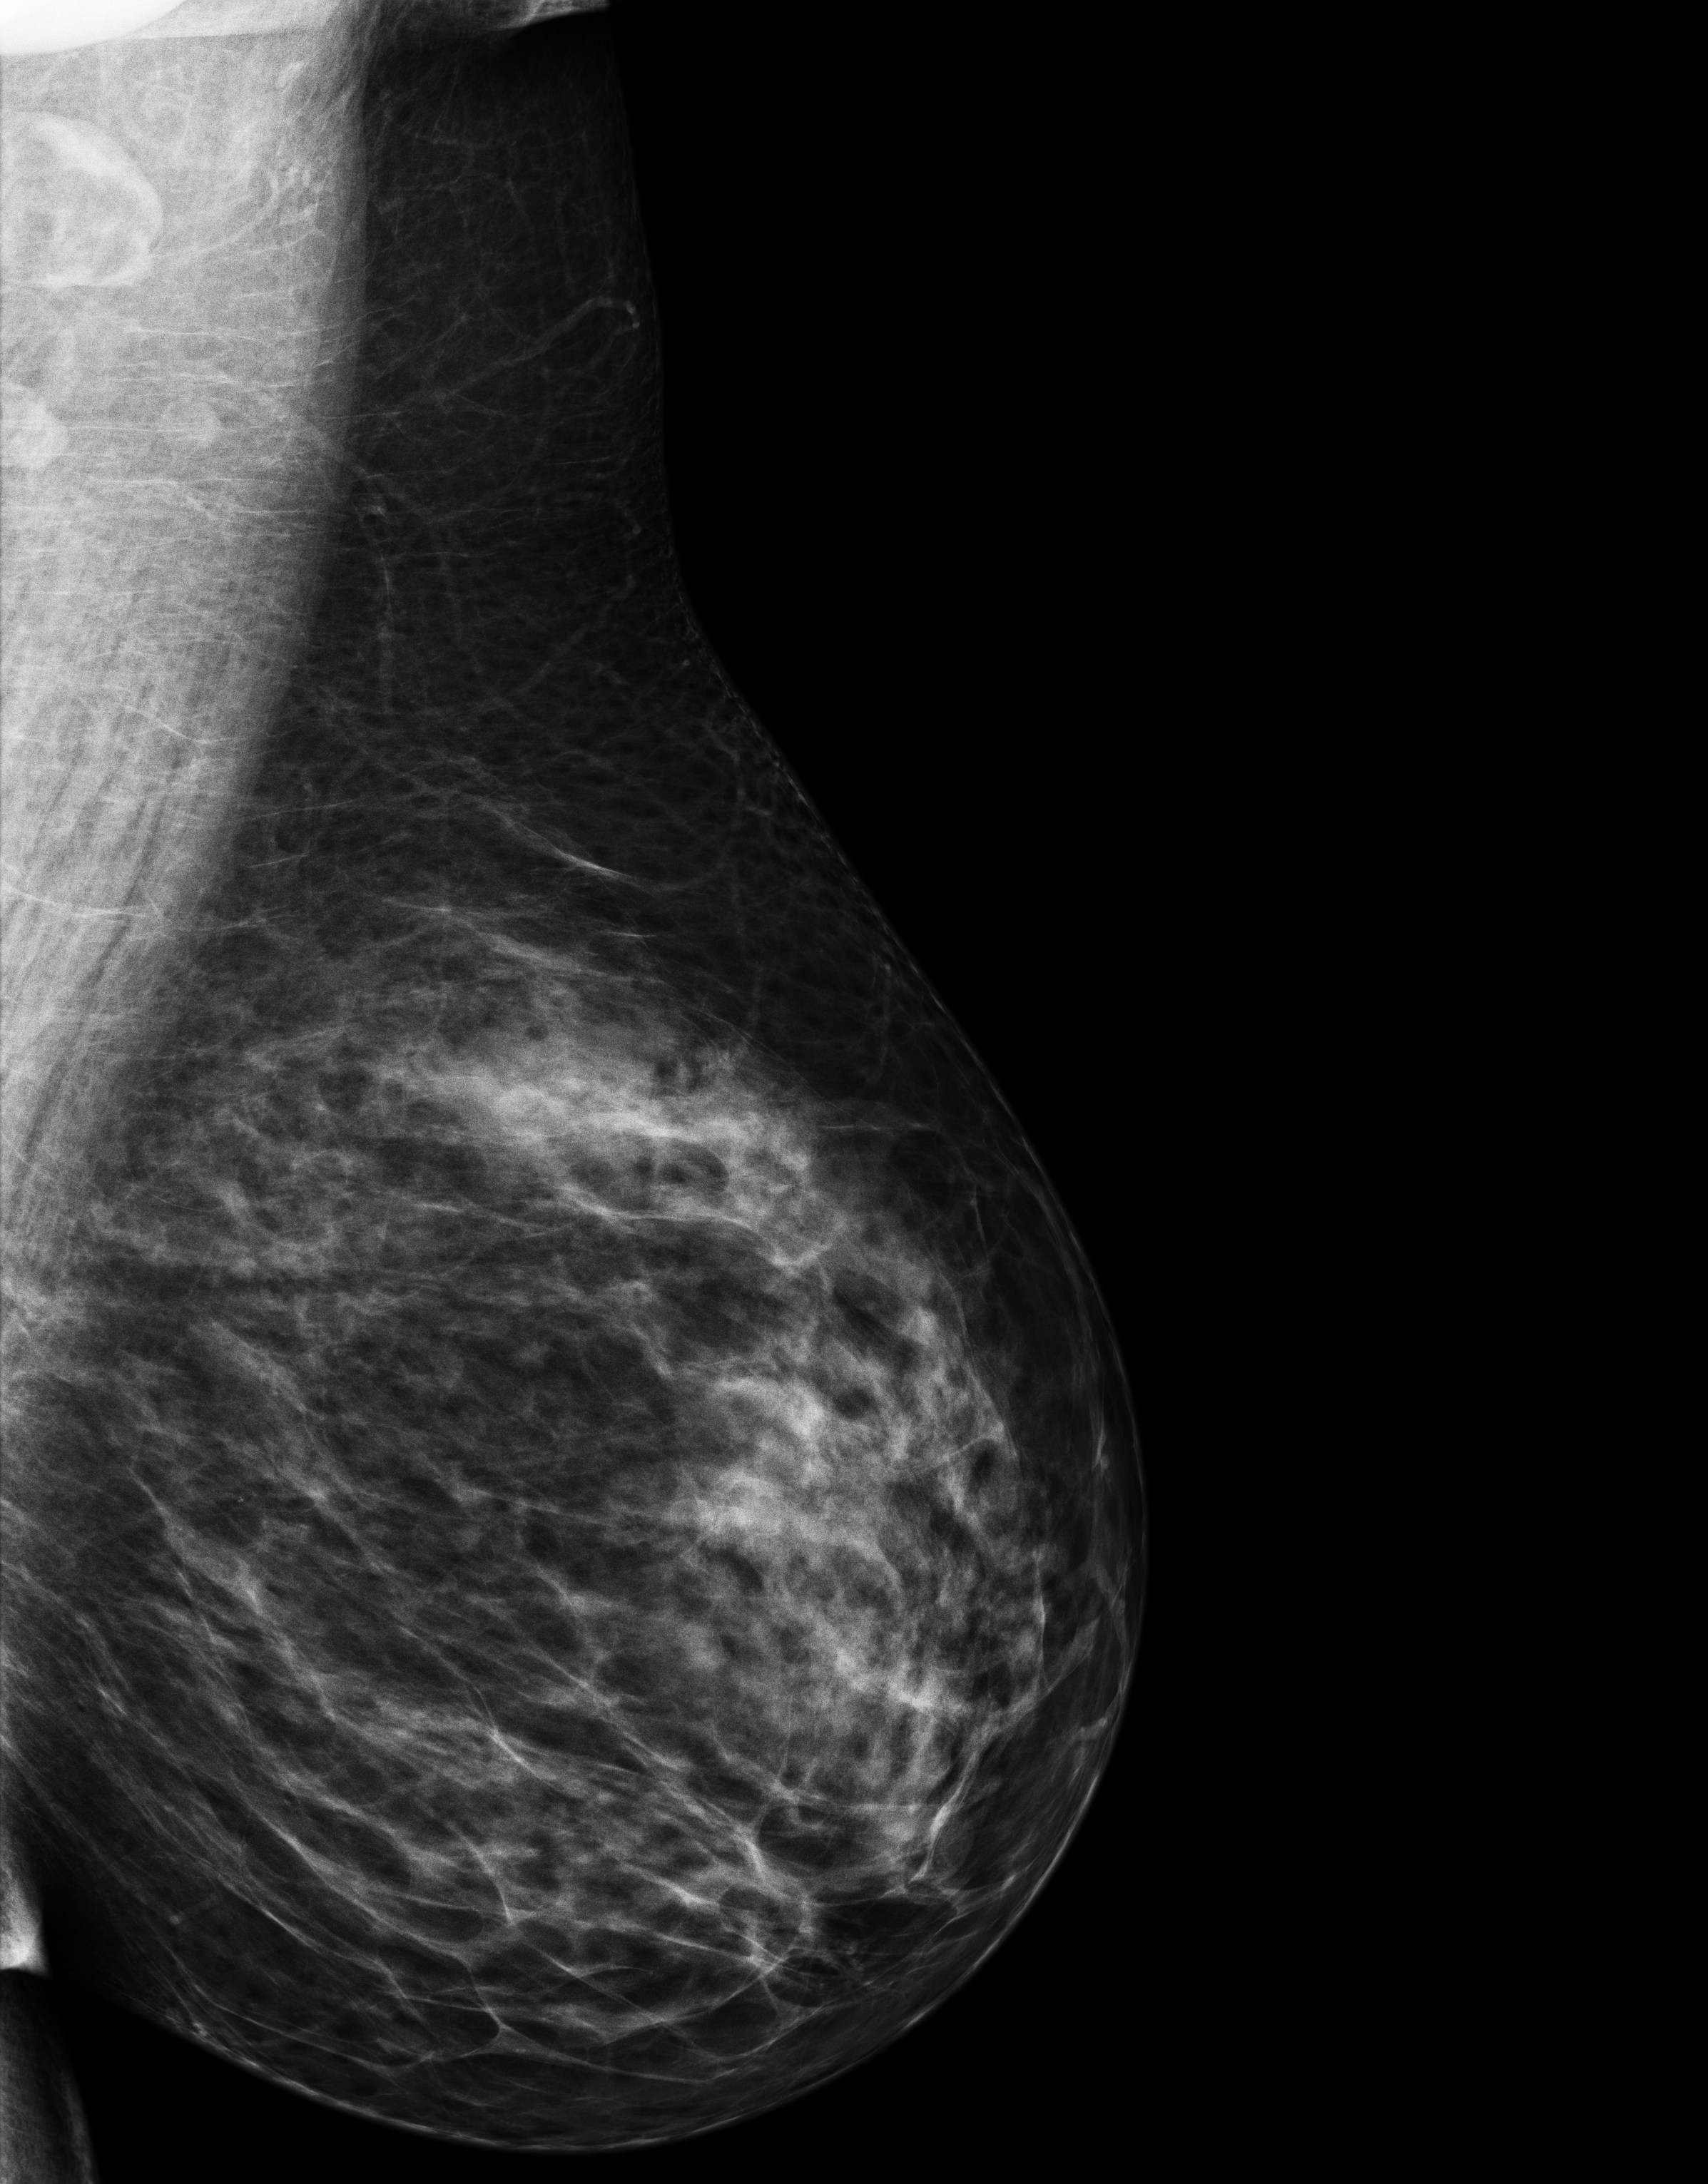
Annual screening mammography examination; system: Senographe Essential ADS_56.21.3. Female patient, age 43 years.
Image type: full-field digital mammogram. Breast: left. Projection: mediolateral oblique (MLO) view.